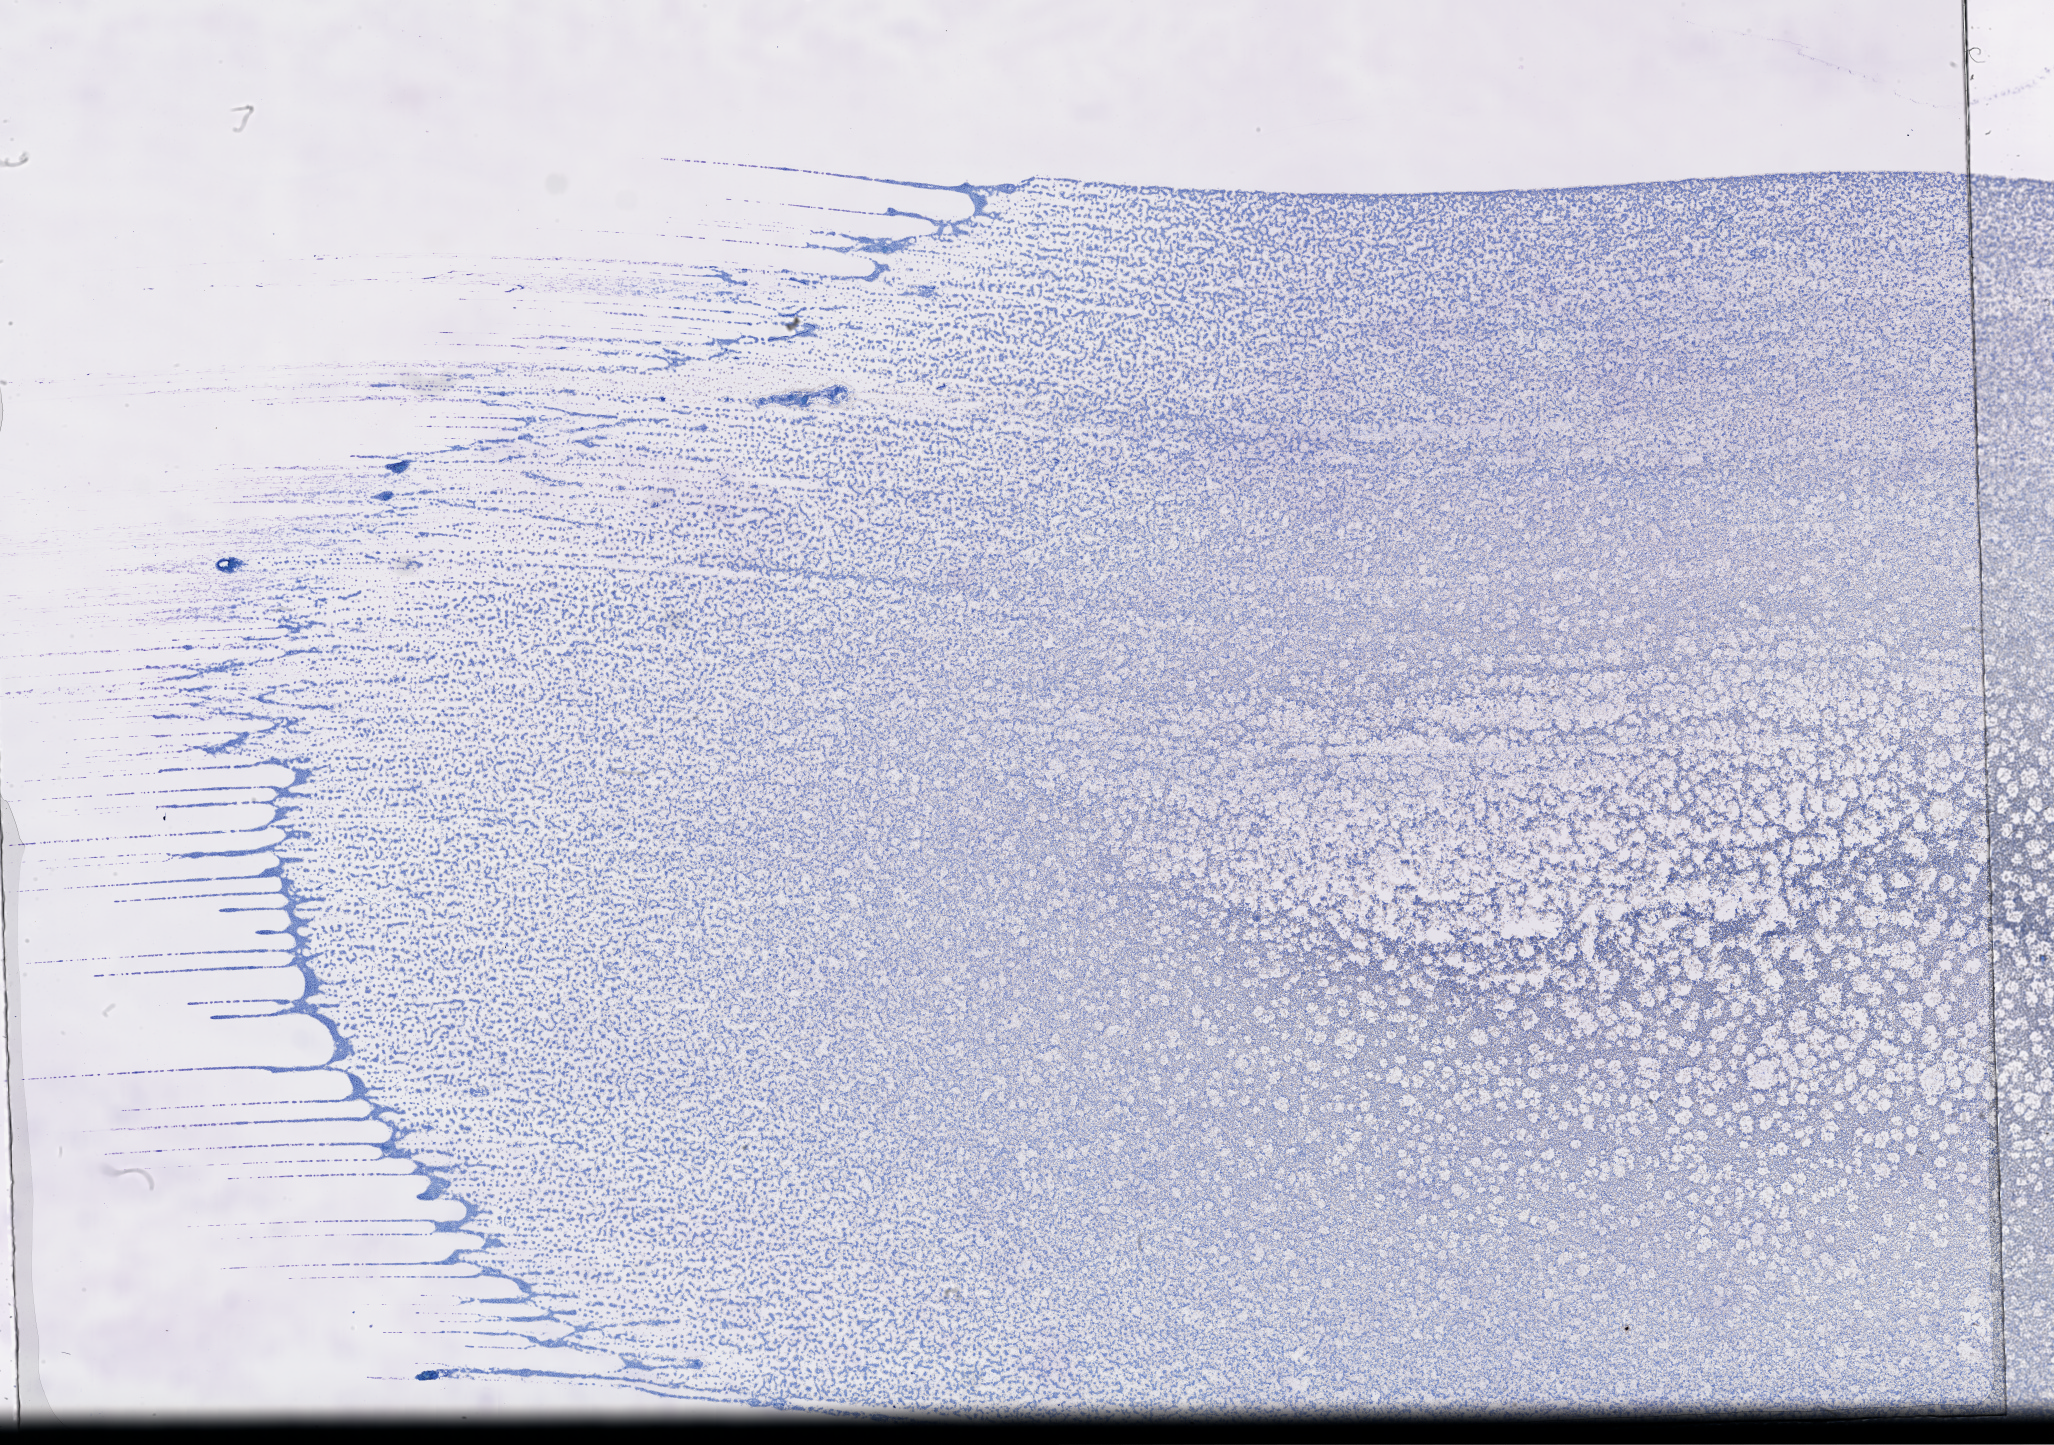
Whole-slide histology image, H&E, whole scanned area (about 33.2 x 23.3 mm) shown as a low-resolution overview. Peripheral blood (leukaemic) sample. Patient: female, age 75 years.
Diagnosis: Acute Myeloid Leukemia. FAB classification: M4. WHO classification: AML with myelodysplasia-related changes.